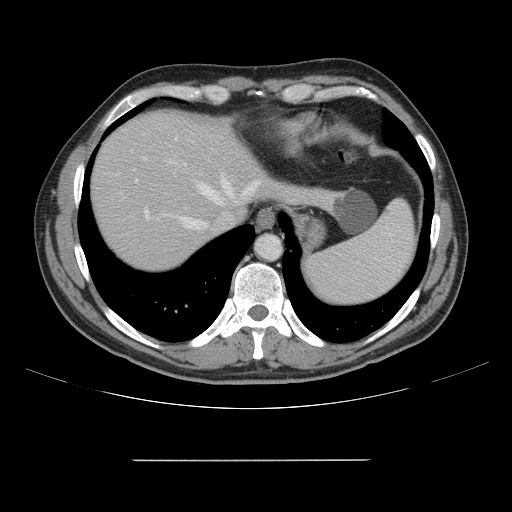
Contrast-enhanced abdominal CT, one axial slice. Slice 131 of 164 in the series (ordered by position). Intravenous contrast given. Soft-tissue window (W 400 / L 40 HU). 2.5 mm slice thickness. 512 × 512 image matrix, field of view 404 × 404 mm. Male patient, age 54 years. Case-level facts recorded for this patient, not image findings: diagnosis: colorectal cancer liver metastases, imaged before liver resection; multiple liver metastases: yes; largest metastasis: 1 cm.
Outlined on this slice (expert manual segmentation):
- hepatic veins: box from (x=164, y=179) to (x=261, y=229) px
- liver: (x=92, y=112)–(x=325, y=272)
- planned liver remnant (the part of the liver to remain after resection): (x=92, y=112)–(x=251, y=272)
- portal vein (with intrahepatic branches): (x=134, y=138)–(x=231, y=219)